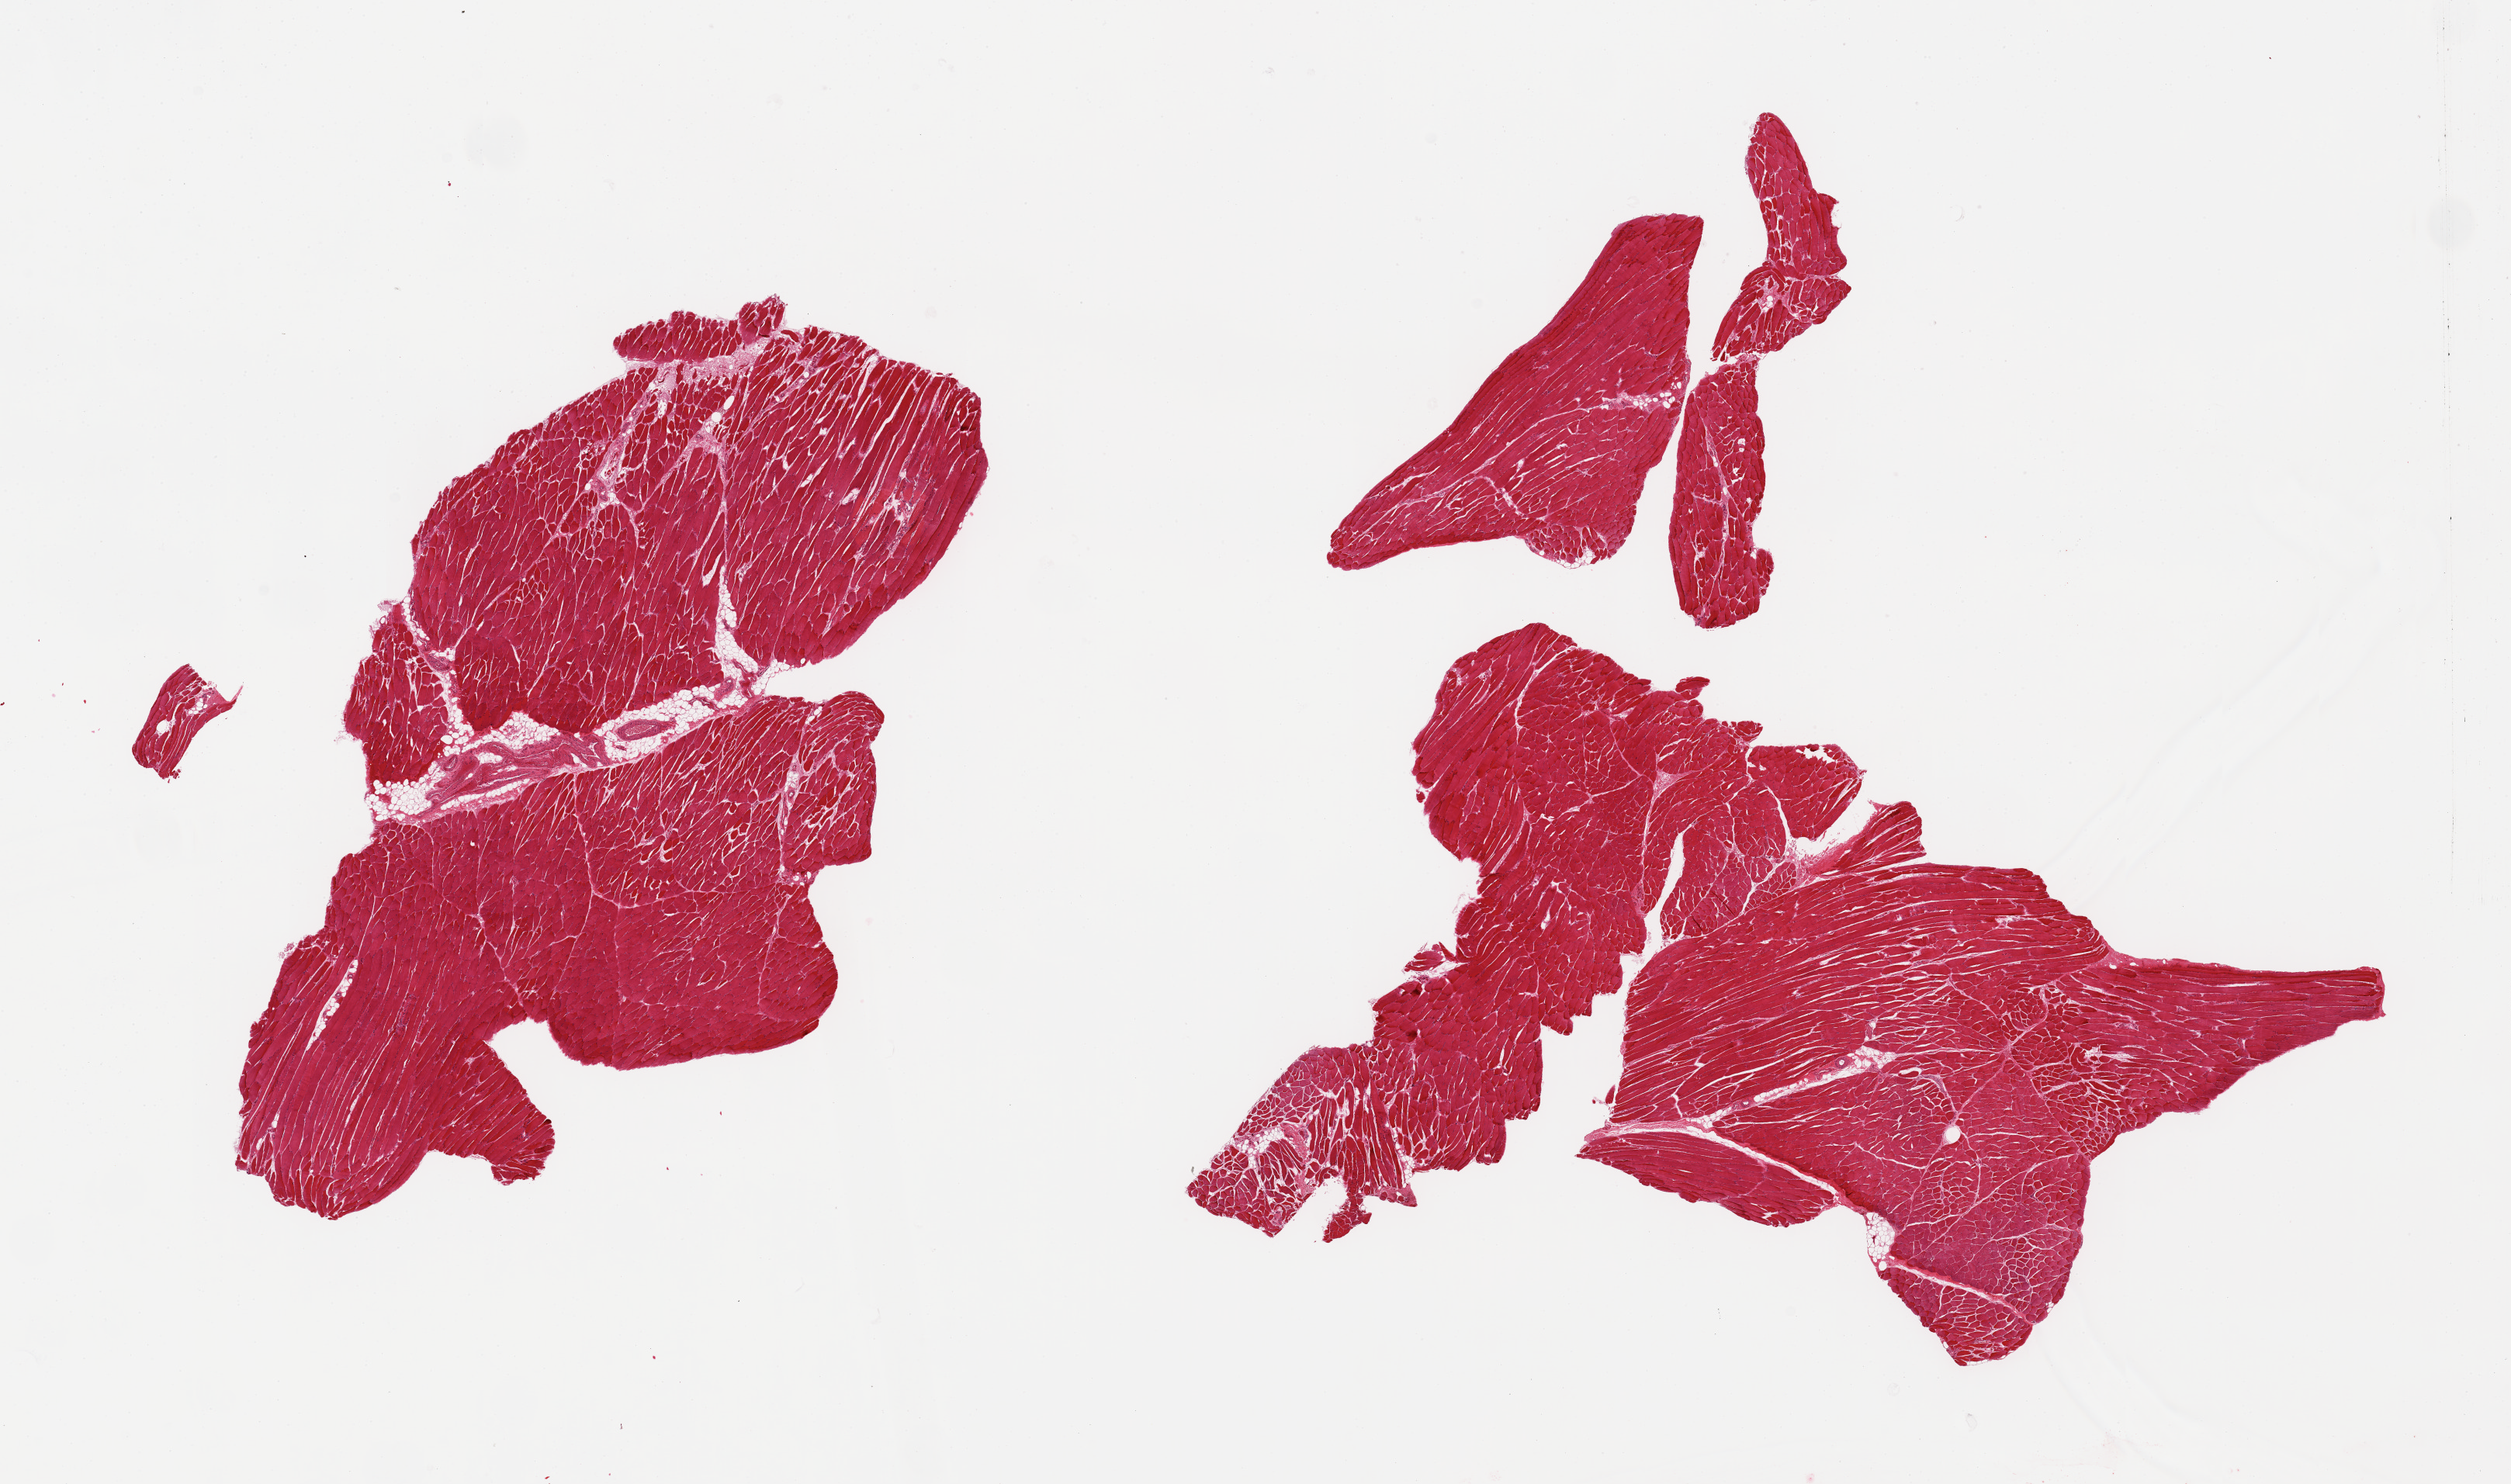
Digitized haematoxylin and eosin-stained section, brightfield, low-resolution overview of the scanned area, about 25.6 x 15.1 mm (slide scanned at 20x), PAXgene-fixed paraffin-embedded (PFPE) section, section of skeletal muscle (target tissue), tissue donor sample. Male donor.
- reviewer comment on this tissue sample: 3 pieces; small central area of fat and vessels in one piece, rare focus of atrophic fibers